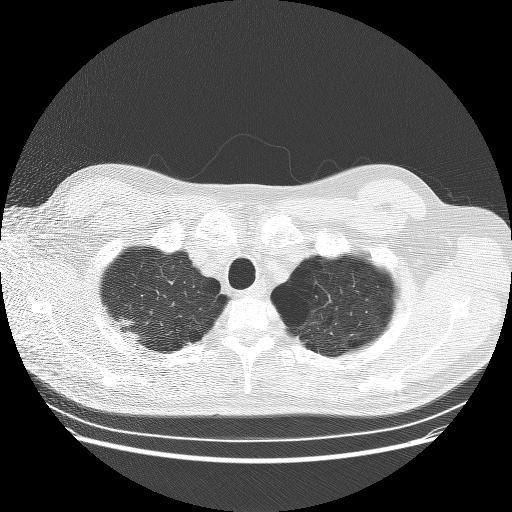
Low-dose screening chest CT, one axial slice. Reconstruction kernel BONE. 120 kVp. Lung window (W 1500 / L -600 HU). 2.5 mm slice thickness. 512 × 512 image matrix, field of view 370 × 370 mm.
Outlined on this slice (outlined manually by an expert reader):
- lesion 1 (tumor, upper lobe of right lung): box from (x=127, y=331) to (x=139, y=339) px